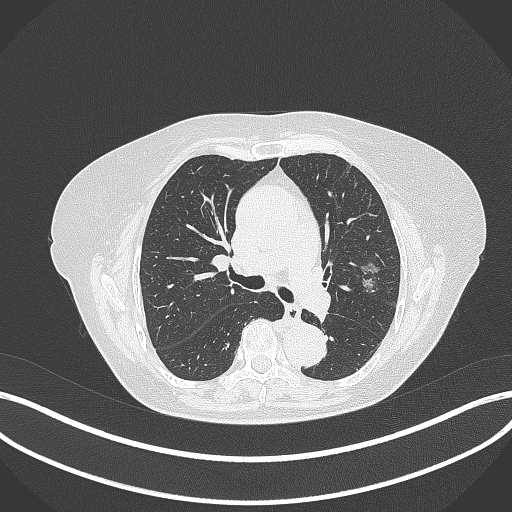
Chest CT, one axial slice; slice 203 of 316 in the series (ordered by position); 120 kVp; lung window (W 1500 / L -600 HU); 512 × 512 image matrix, field of view 400 × 400 mm. Patient: female, 75 years. Case-level facts recorded for this patient, not image findings: clinical TNM (as recorded): T1c N0 M0.
Annotated regions visible in this slice (rectangle marked by the reading radiologist):
- lung tumour (recorded histology: adenocarcinoma): bounding box [x1, y1, x2, y2] px = [353, 261, 383, 295]